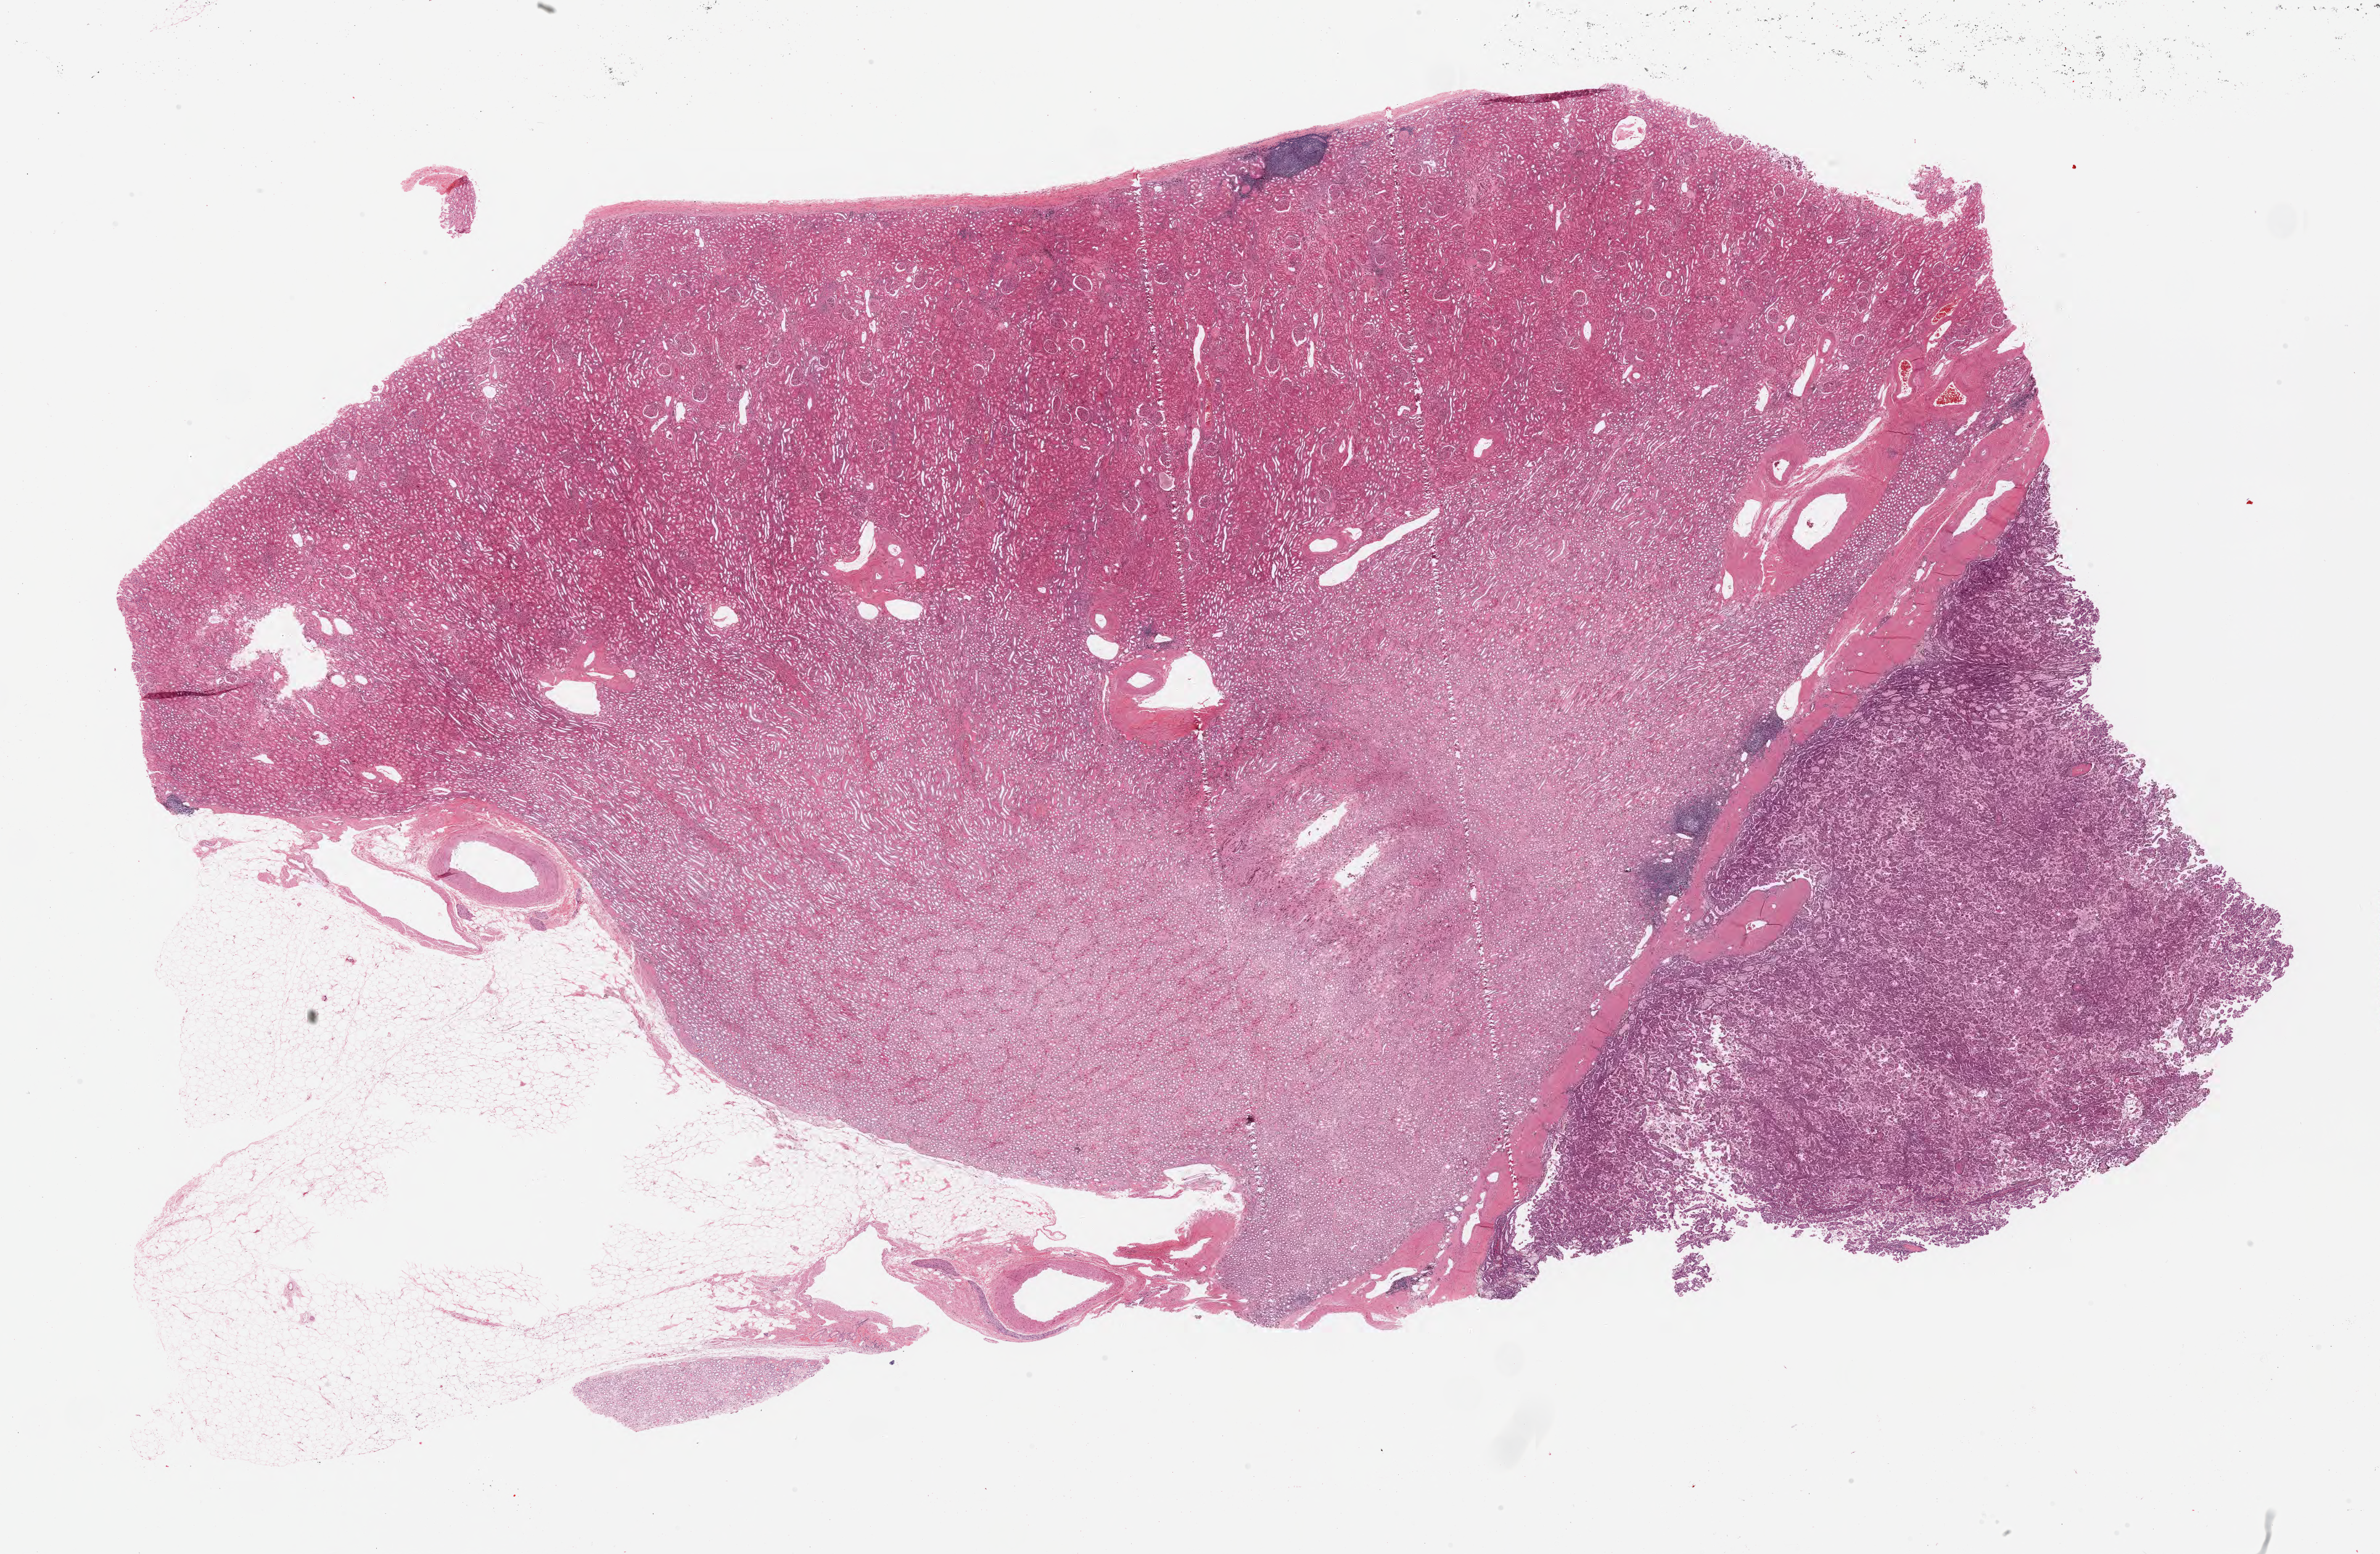
H&E whole-slide image, low-resolution overview of the scanned area, about 30.5 x 19.9 mm (from a 20x scan); formalin-fixed paraffin-embedded (FFPE) diagnostic section; kidney, primary tumour sample. Male patient; age at initial diagnosis 70 years.
Pathologic diagnosis: Papillary adenocarcinoma, NOS.